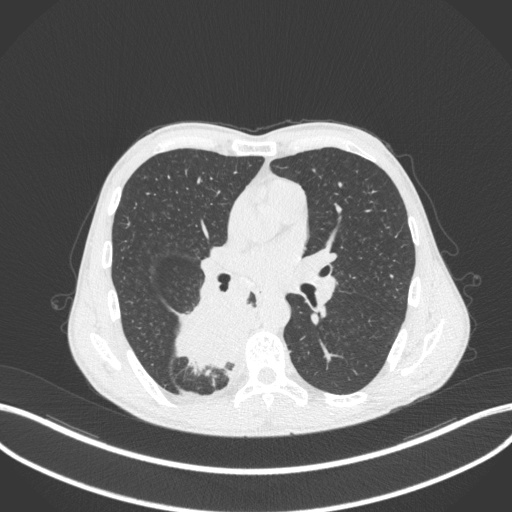
Chest CT, one axial slice; slice 202 of 371 in the series (ordered by position); 120 kVp; lung window (W 1500 / L -600 HU); 1 mm slice thickness; 512 × 512 image matrix. Male patient, age 58 years. From the clinical record (not read from this slice): clinical TNM (as recorded): T3 N1 M1.
Annotated regions visible in this slice (rectangle marked by the reading radiologist):
- lung tumour (recorded histology: squamous cell carcinoma): bounding box [x1, y1, x2, y2] px = [169, 296, 261, 382]